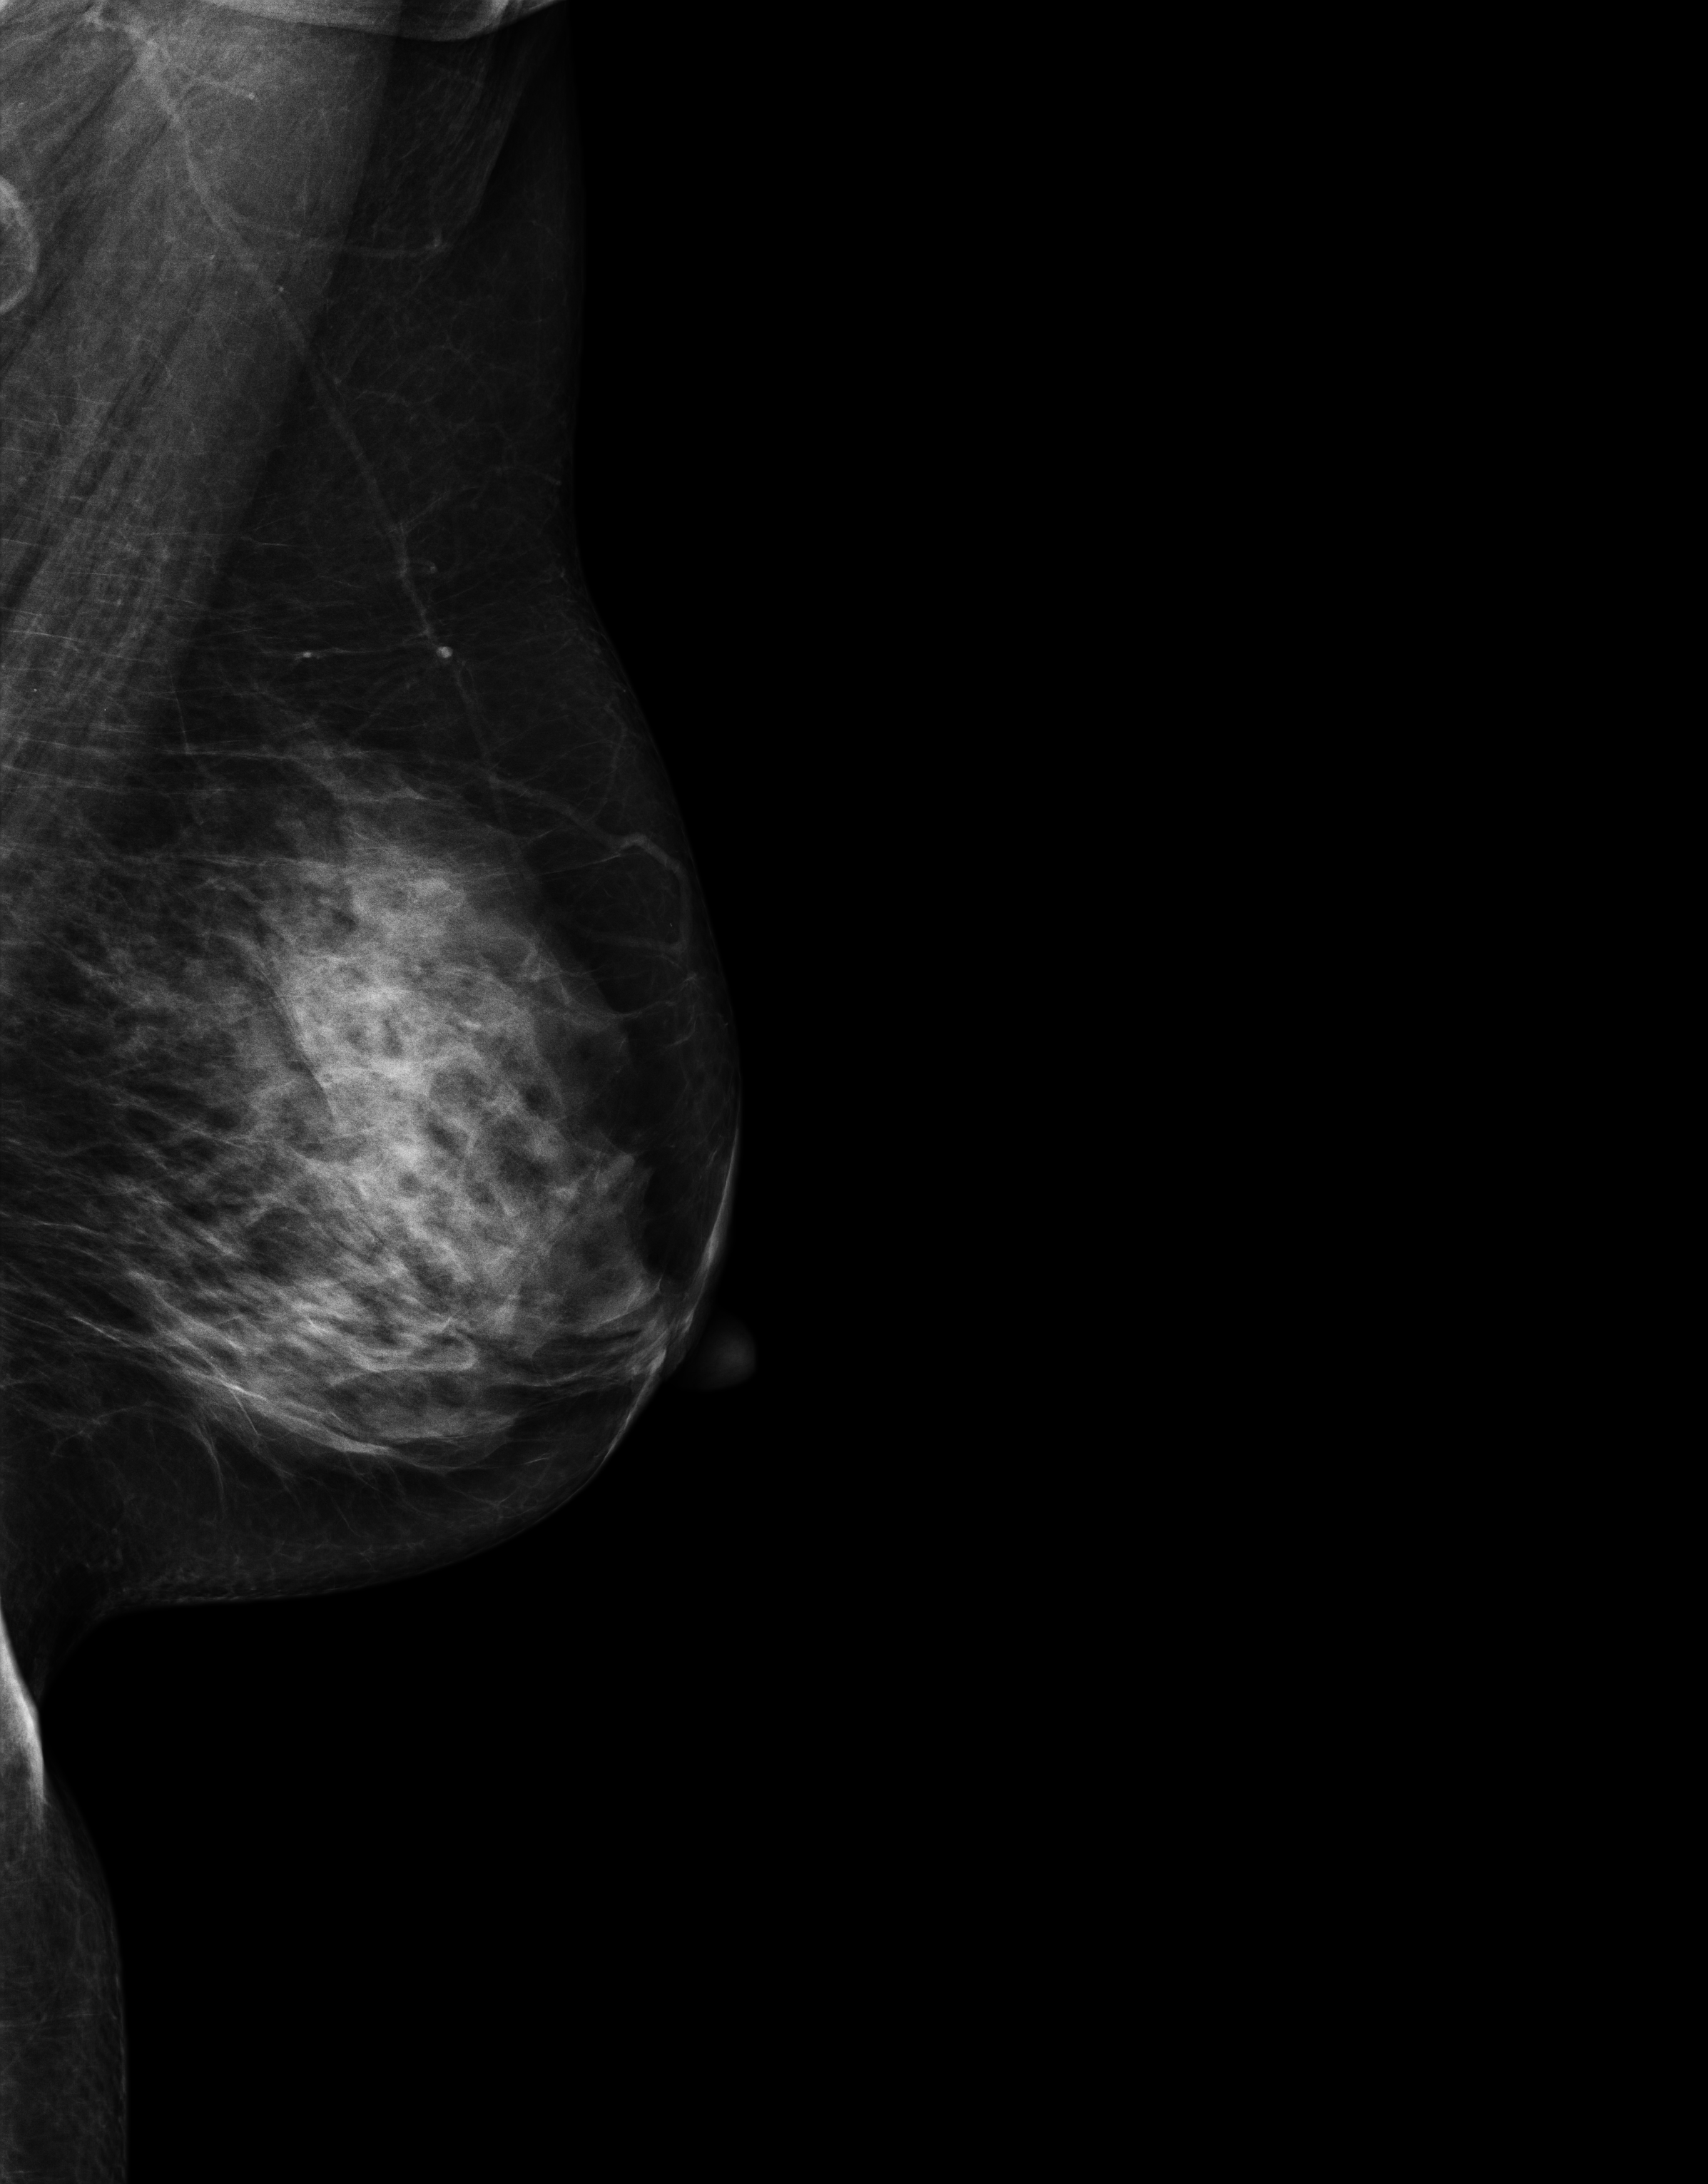
Full-field digital mammogram (FFDM), left breast, MLO view, screening examination. Female patient, age 67 years.
- breast density at the screening exam (both breasts): heterogeneously dense (BI-RADS density category c)
- final BI-RADS assessment for this screening round (tomosynthesis exam, both breasts): category 1
- recall: no recall after this screen